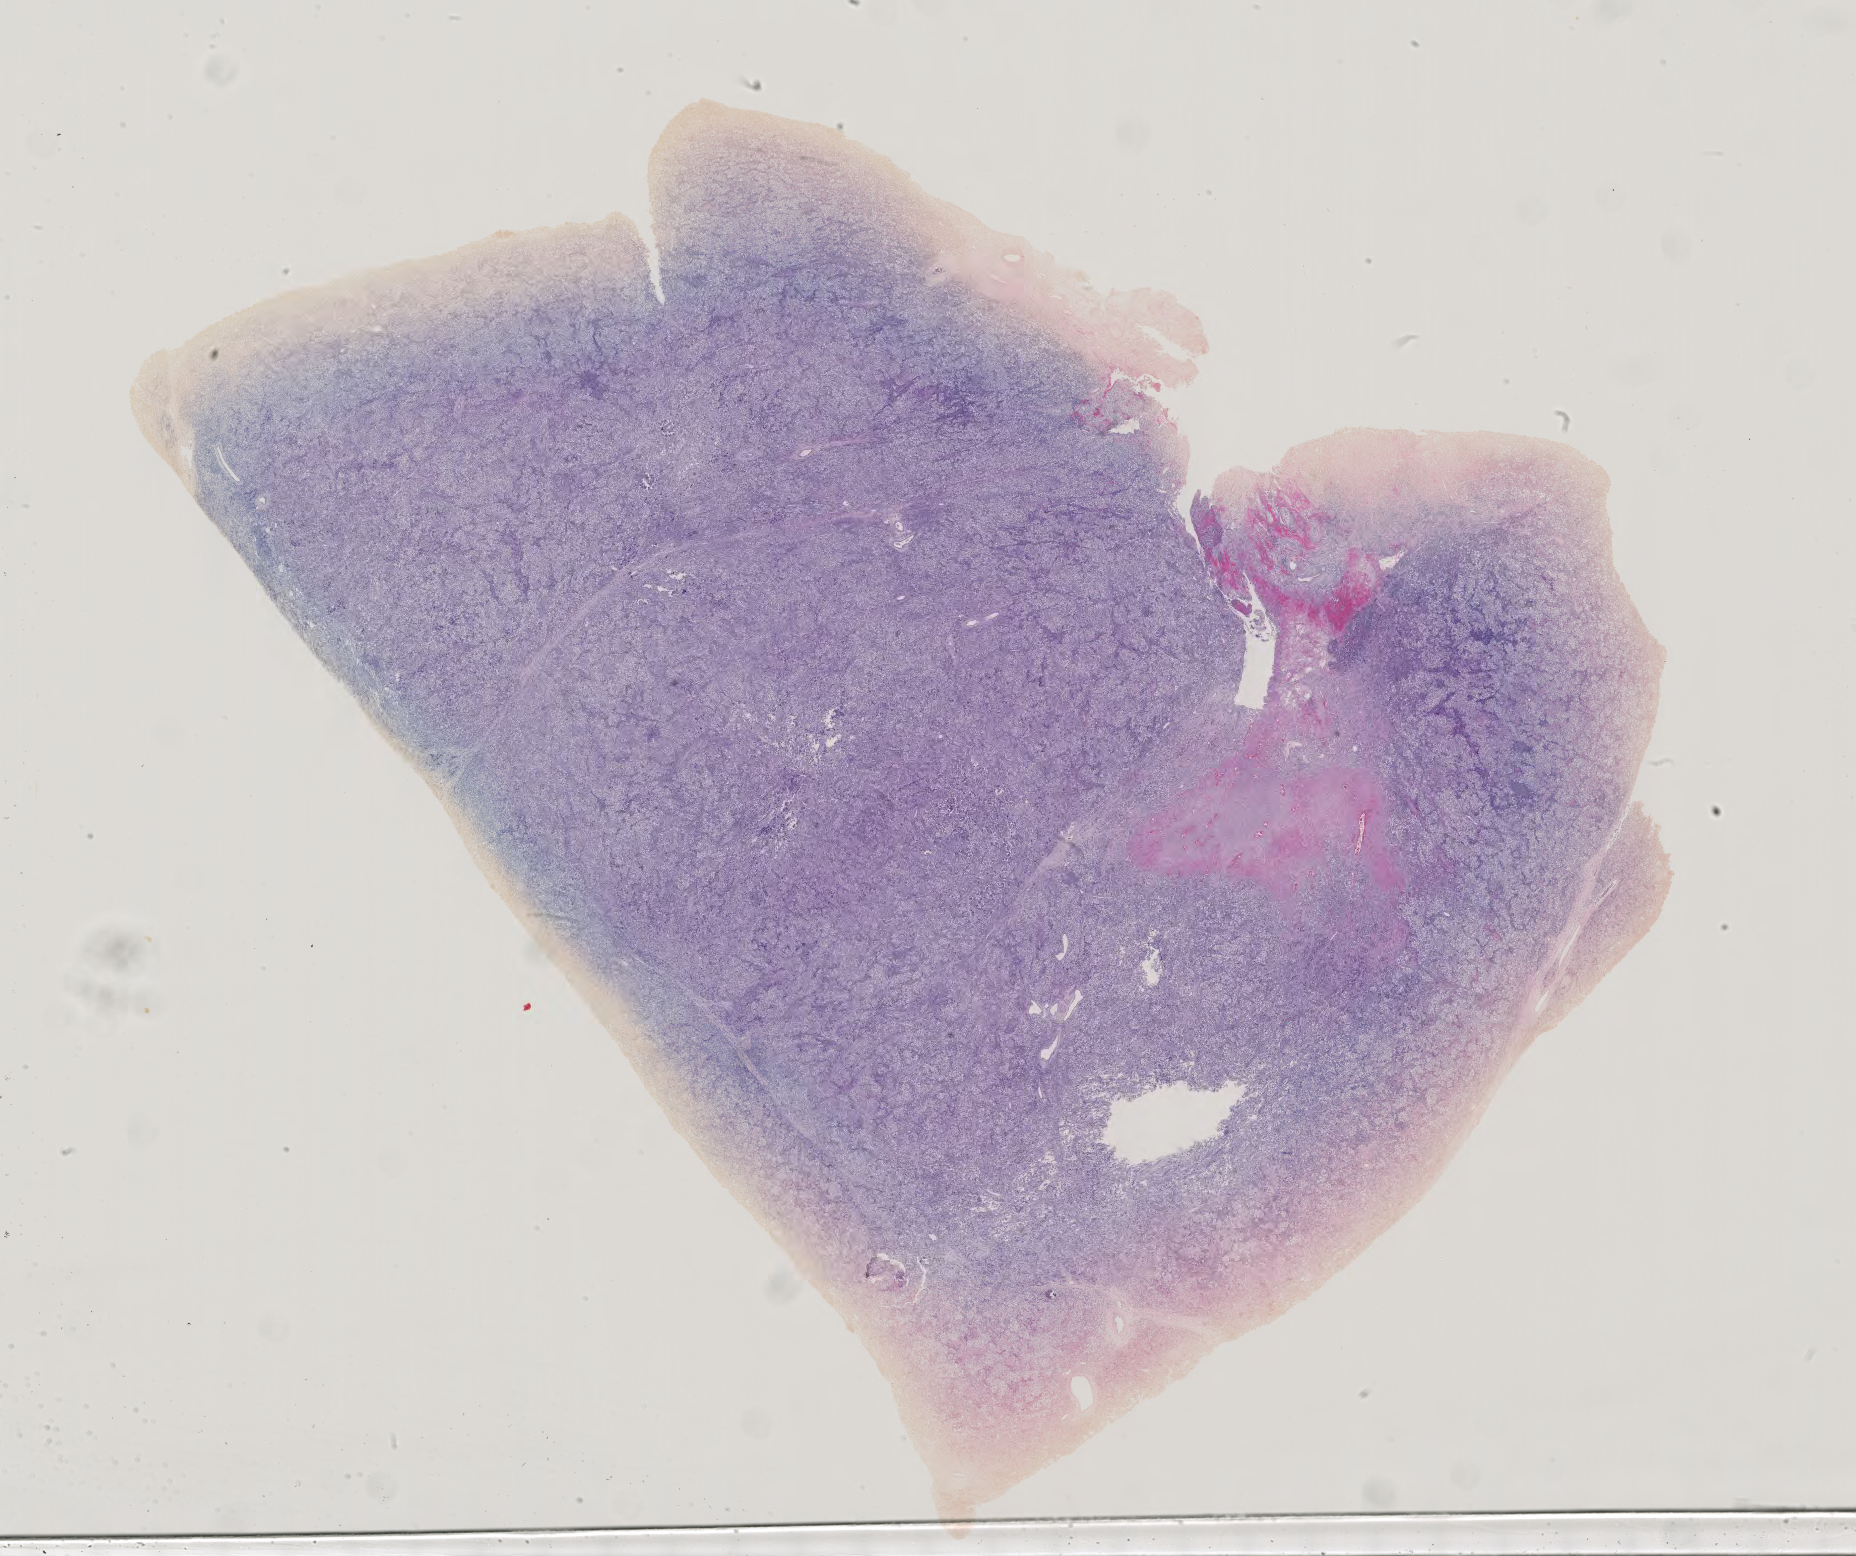
Hematoxylin and eosin (H&E) stained whole-slide image — a low-resolution overview of the entire scanned area, about 27.0 x 22.7 mm (acquisition: 40x scan). Patient sex: male.
Specimen: formalin-fixed paraffin-embedded (FFPE) diagnostic section; primary tumour sample from the testis.